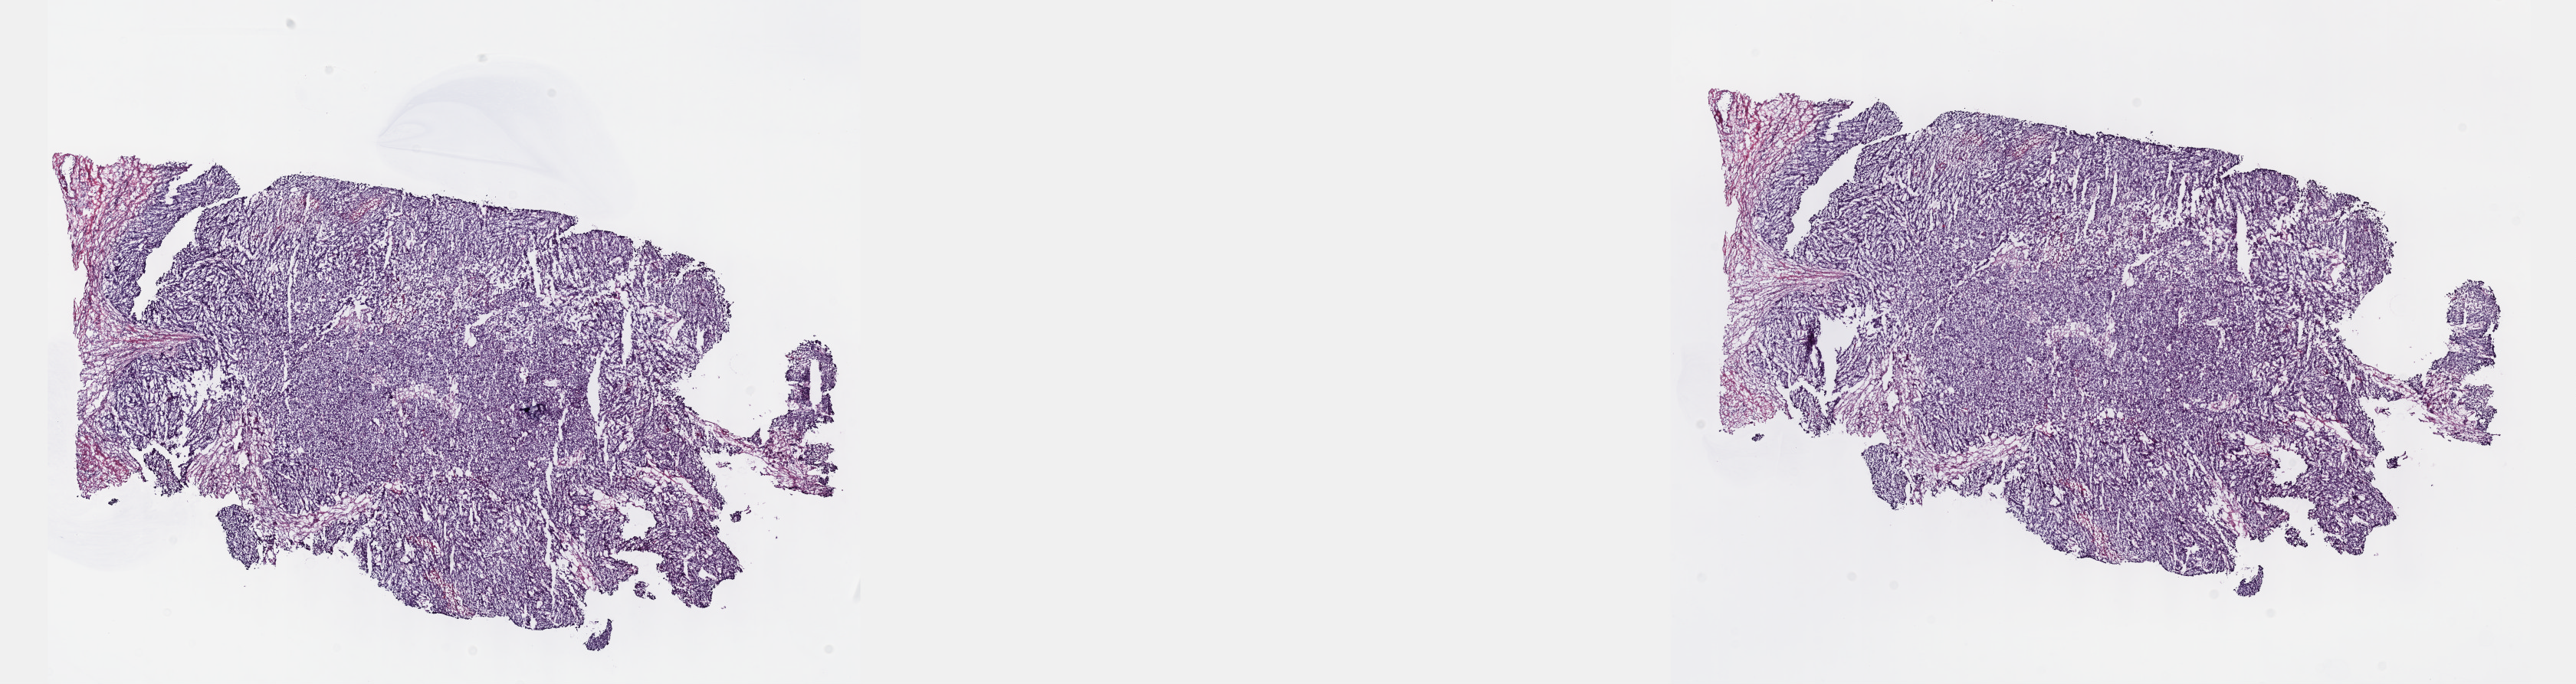
Whole-slide histology image, Hematoxylin and eosin (H&E) stained, shown as a low-resolution overview of the whole scanned area (about 27.2 x 7.2 mm), frozen section from the top of the tissue portion, bladder, primary tumour sample. Male, age 68 years at initial diagnosis. Histologic grade: high grade. Composition of this section per pathologist review: tumour cells 75%, tumour nuclei 75%, normal cells 0%, stromal cells 25%, necrosis 0%. Infiltration values recorded for this section: lymphocyte infiltration 2%, monocyte infiltration 1%, neutrophil infiltration 4%.
- AJCC pathologic stage: III
- lymph nodes positive (case pathology): 0 of 13 examined
- histologic diagnosis: Papillary transitional cell carcinoma